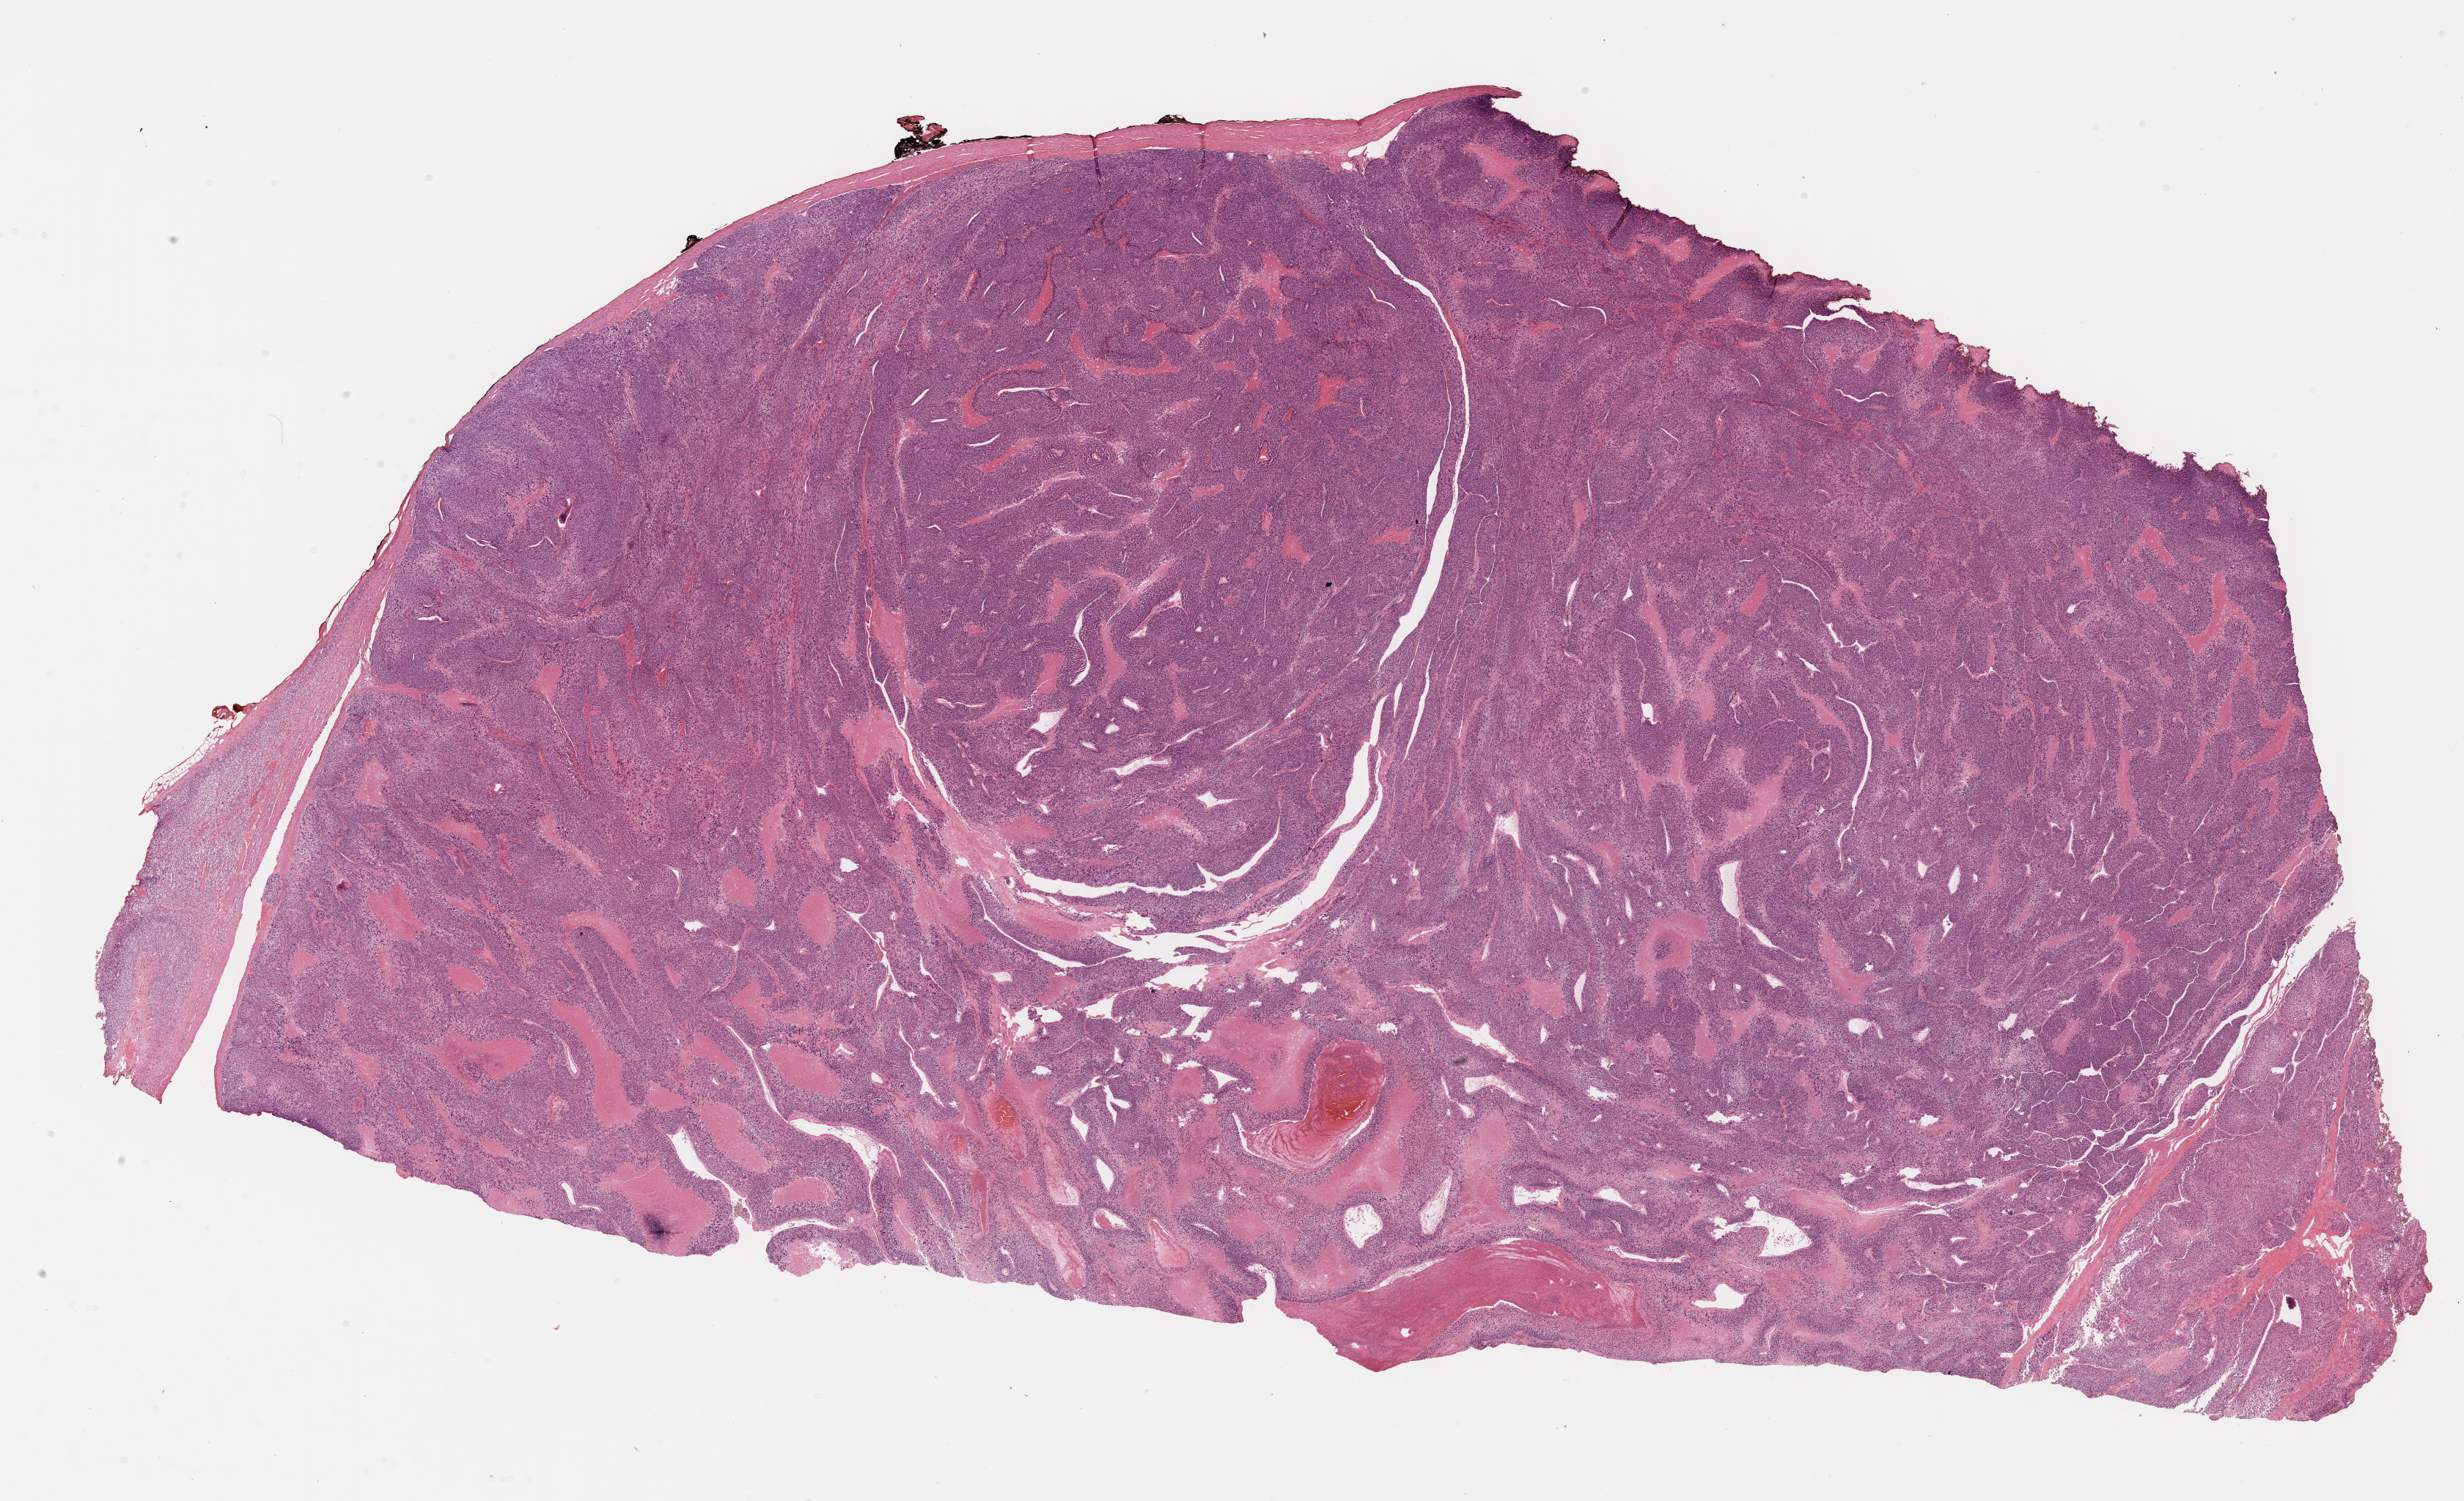
Whole-slide histology image, H&E, low-resolution overview of the scanned area, about 27.2 x 16.6 mm (from a 40x scan). Formalin-fixed paraffin-embedded (FFPE) diagnostic section. Adrenal cortex, primary tumour sample. Female patient; age at initial diagnosis 25 years.
- histologic diagnosis: Adrenal cortical carcinoma (cortex of adrenal gland)